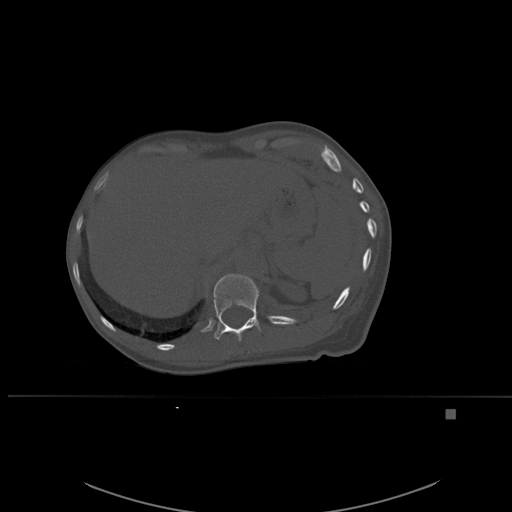
CT including the spine, one axial slice; position 281 of 537 along the scan axis; bone window (W 1800 / L 400 HU); 1.5 mm slice thickness; 512 × 512 image matrix, field of view 440 × 440 mm. Female patient, age 45 years. Case-level facts recorded for this patient, not image findings: primary cancer: lung.
Structures marked on this image (semi-automatically segmented with operator editing):
- T12 vertebra: bounding box <213,274,261,342> (left, top, right, bottom; pixels)